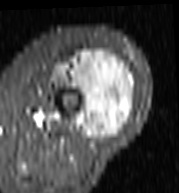
MRI of an extremity soft-tissue mass, one axial slice. Position 46 of 103 along the scan axis. STIR. MR volume resampled by the dataset authors to the PET/CT grid (not the native acquisition matrix). 3.27 mm slice thickness. 179 × 193 image matrix, field of view 175 × 188 mm. Female patient. From the clinical record (not read from this slice): histological type: undifferentiated – high grade; grade: high; site of the primary tumour: left thigh.
Structures marked on this image (expert contour drawn on MRI and transferred to this co-registered scan by the dataset authors):
- gross tumour volume including surrounding oedema: box from (x=54, y=51) to (x=137, y=139) px
- gross tumour volume (mass): (x=66, y=51)–(x=135, y=139)